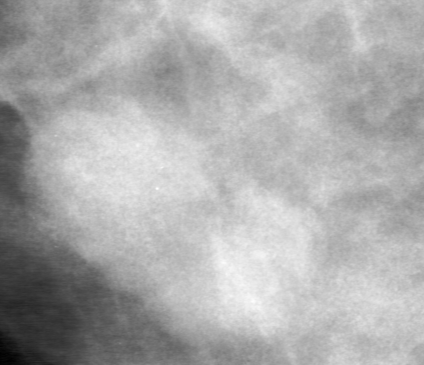
Cropped region of a digitized screen-film mammogram centred on a radiologist-marked abnormality, right breast, MLO view, BI-RADS breast density category 2 (scale 1–4).
- Mass, shape oval, margins obscured; BI-RADS assessment category 0 (incomplete: needs additional imaging); subtlety rating 4 on a 1 (subtle) to 5 (obvious) scale; pathology result (as recorded, not read from the image): benign.